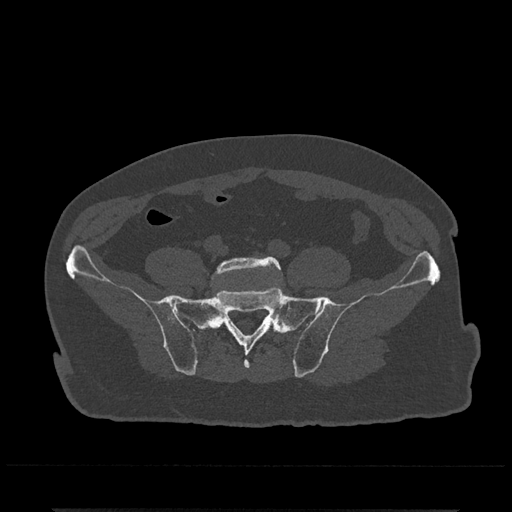
CT including the spine, one axial slice; reconstruction kernel Br40s/3; bone window (W 1800 / L 400 HU); 0.5 mm slice thickness; 512 × 512 image matrix, field of view 393 × 393 mm. Patient: male, 67 years. From the clinical record (not read from this slice): primary cancer: prostate.
Annotated regions visible in this slice (semi-automatically segmented with operator editing):
- L5 vertebra: bounding box [x1, y1, x2, y2] px = [212, 256, 283, 291]